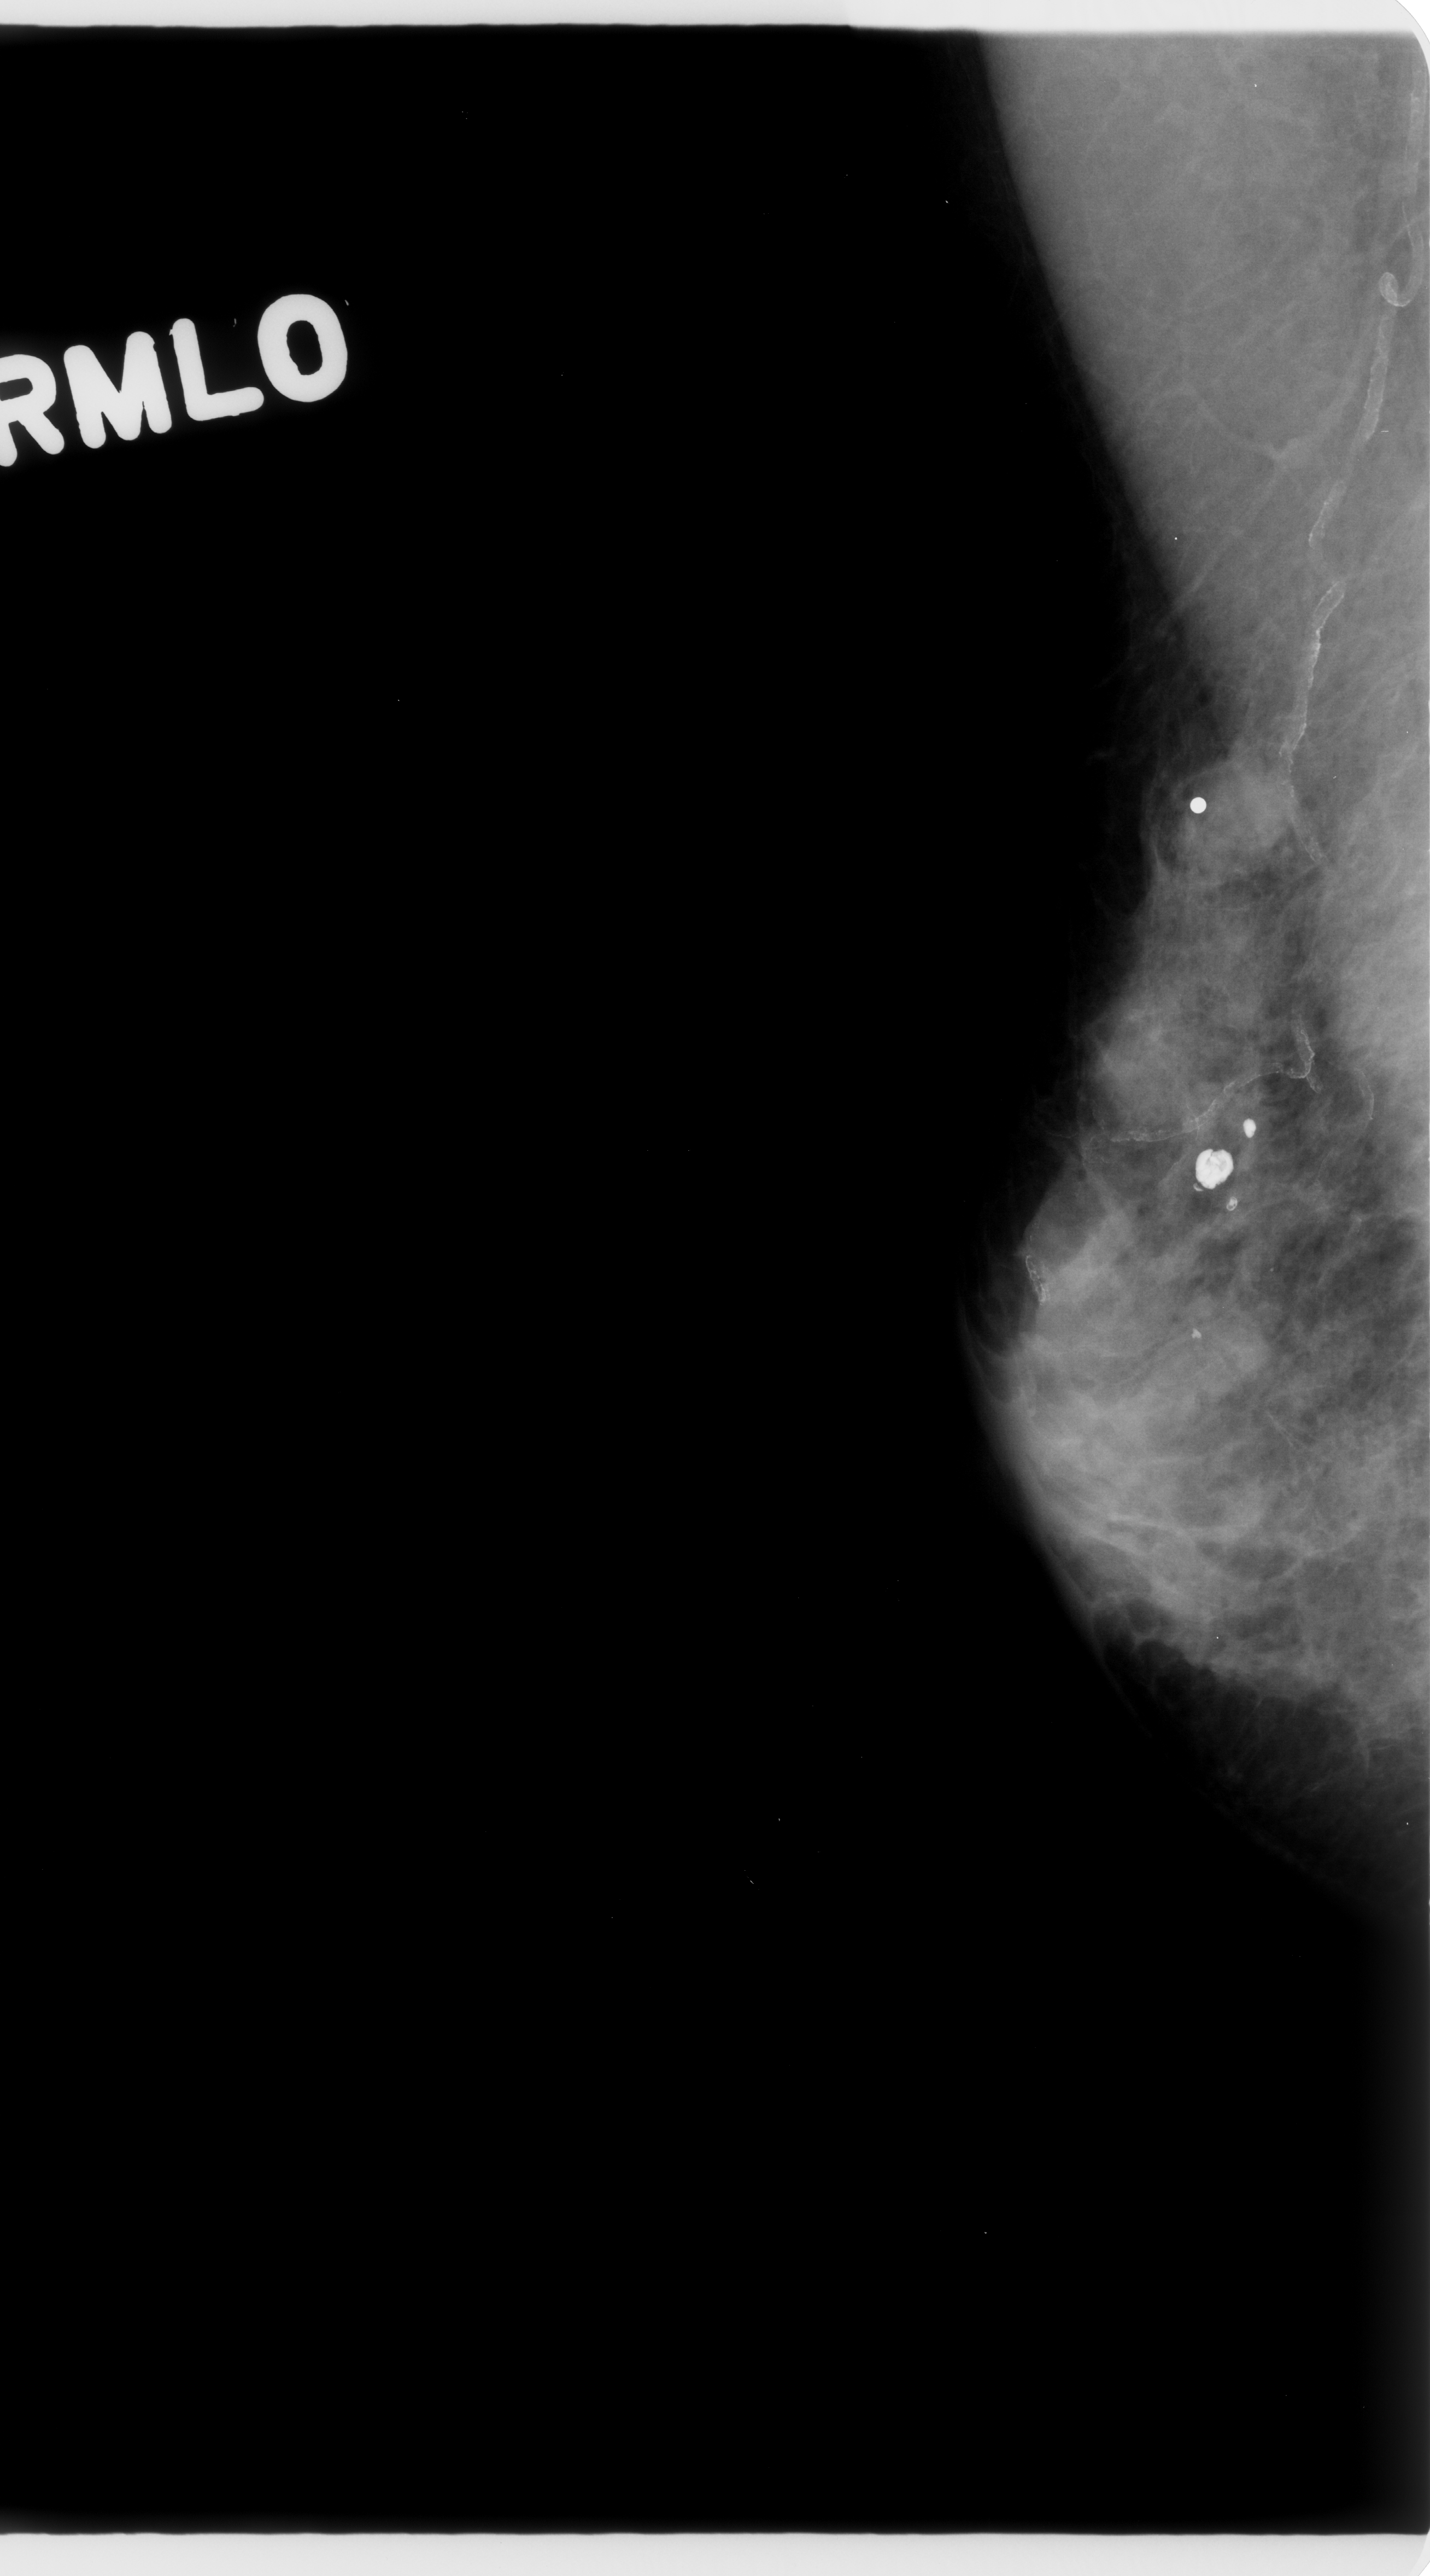
Mammogram (digitized film). Right breast. Mediolateral oblique (MLO) view. BI-RADS breast density category 3 (scale 1–4). 1430 × 2576 image matrix.
Expert-marked regions of interest on this image (one box per marked abnormality):
- mass, shape oval, margins circumscribed; BI-RADS assessment category 4; subtlety rating 4 on a 1 (subtle) to 5 (obvious) scale; pathology (as recorded): malignant: box from (x=1167, y=731) to (x=1312, y=880) px